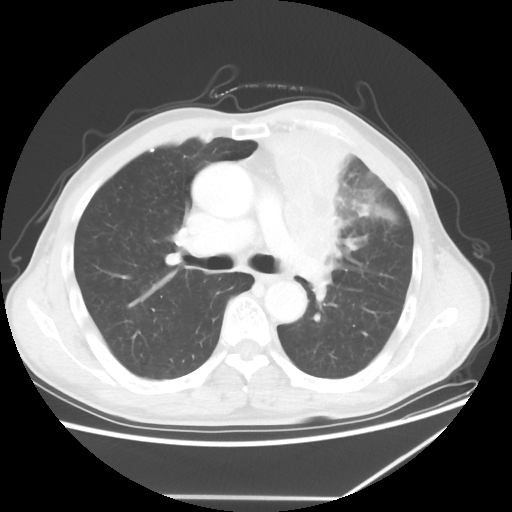
Chest CT, one axial slice. Position 39 of 64 along the scan axis. 100 kVp. Lung window (W 1500 / L -600 HU). 5 mm slice thickness. 512 × 512 image matrix, field of view 383 × 383 mm. Patient: male, 64 years. From the clinical record (not read from this slice): clinical TNM (as recorded): T1c N1 M1.
Structures marked on this image (bounding box drawn by a radiologist):
- lung tumour (recorded histology: squamous cell carcinoma): bounding box <237,107,388,282> (left, top, right, bottom; pixels)